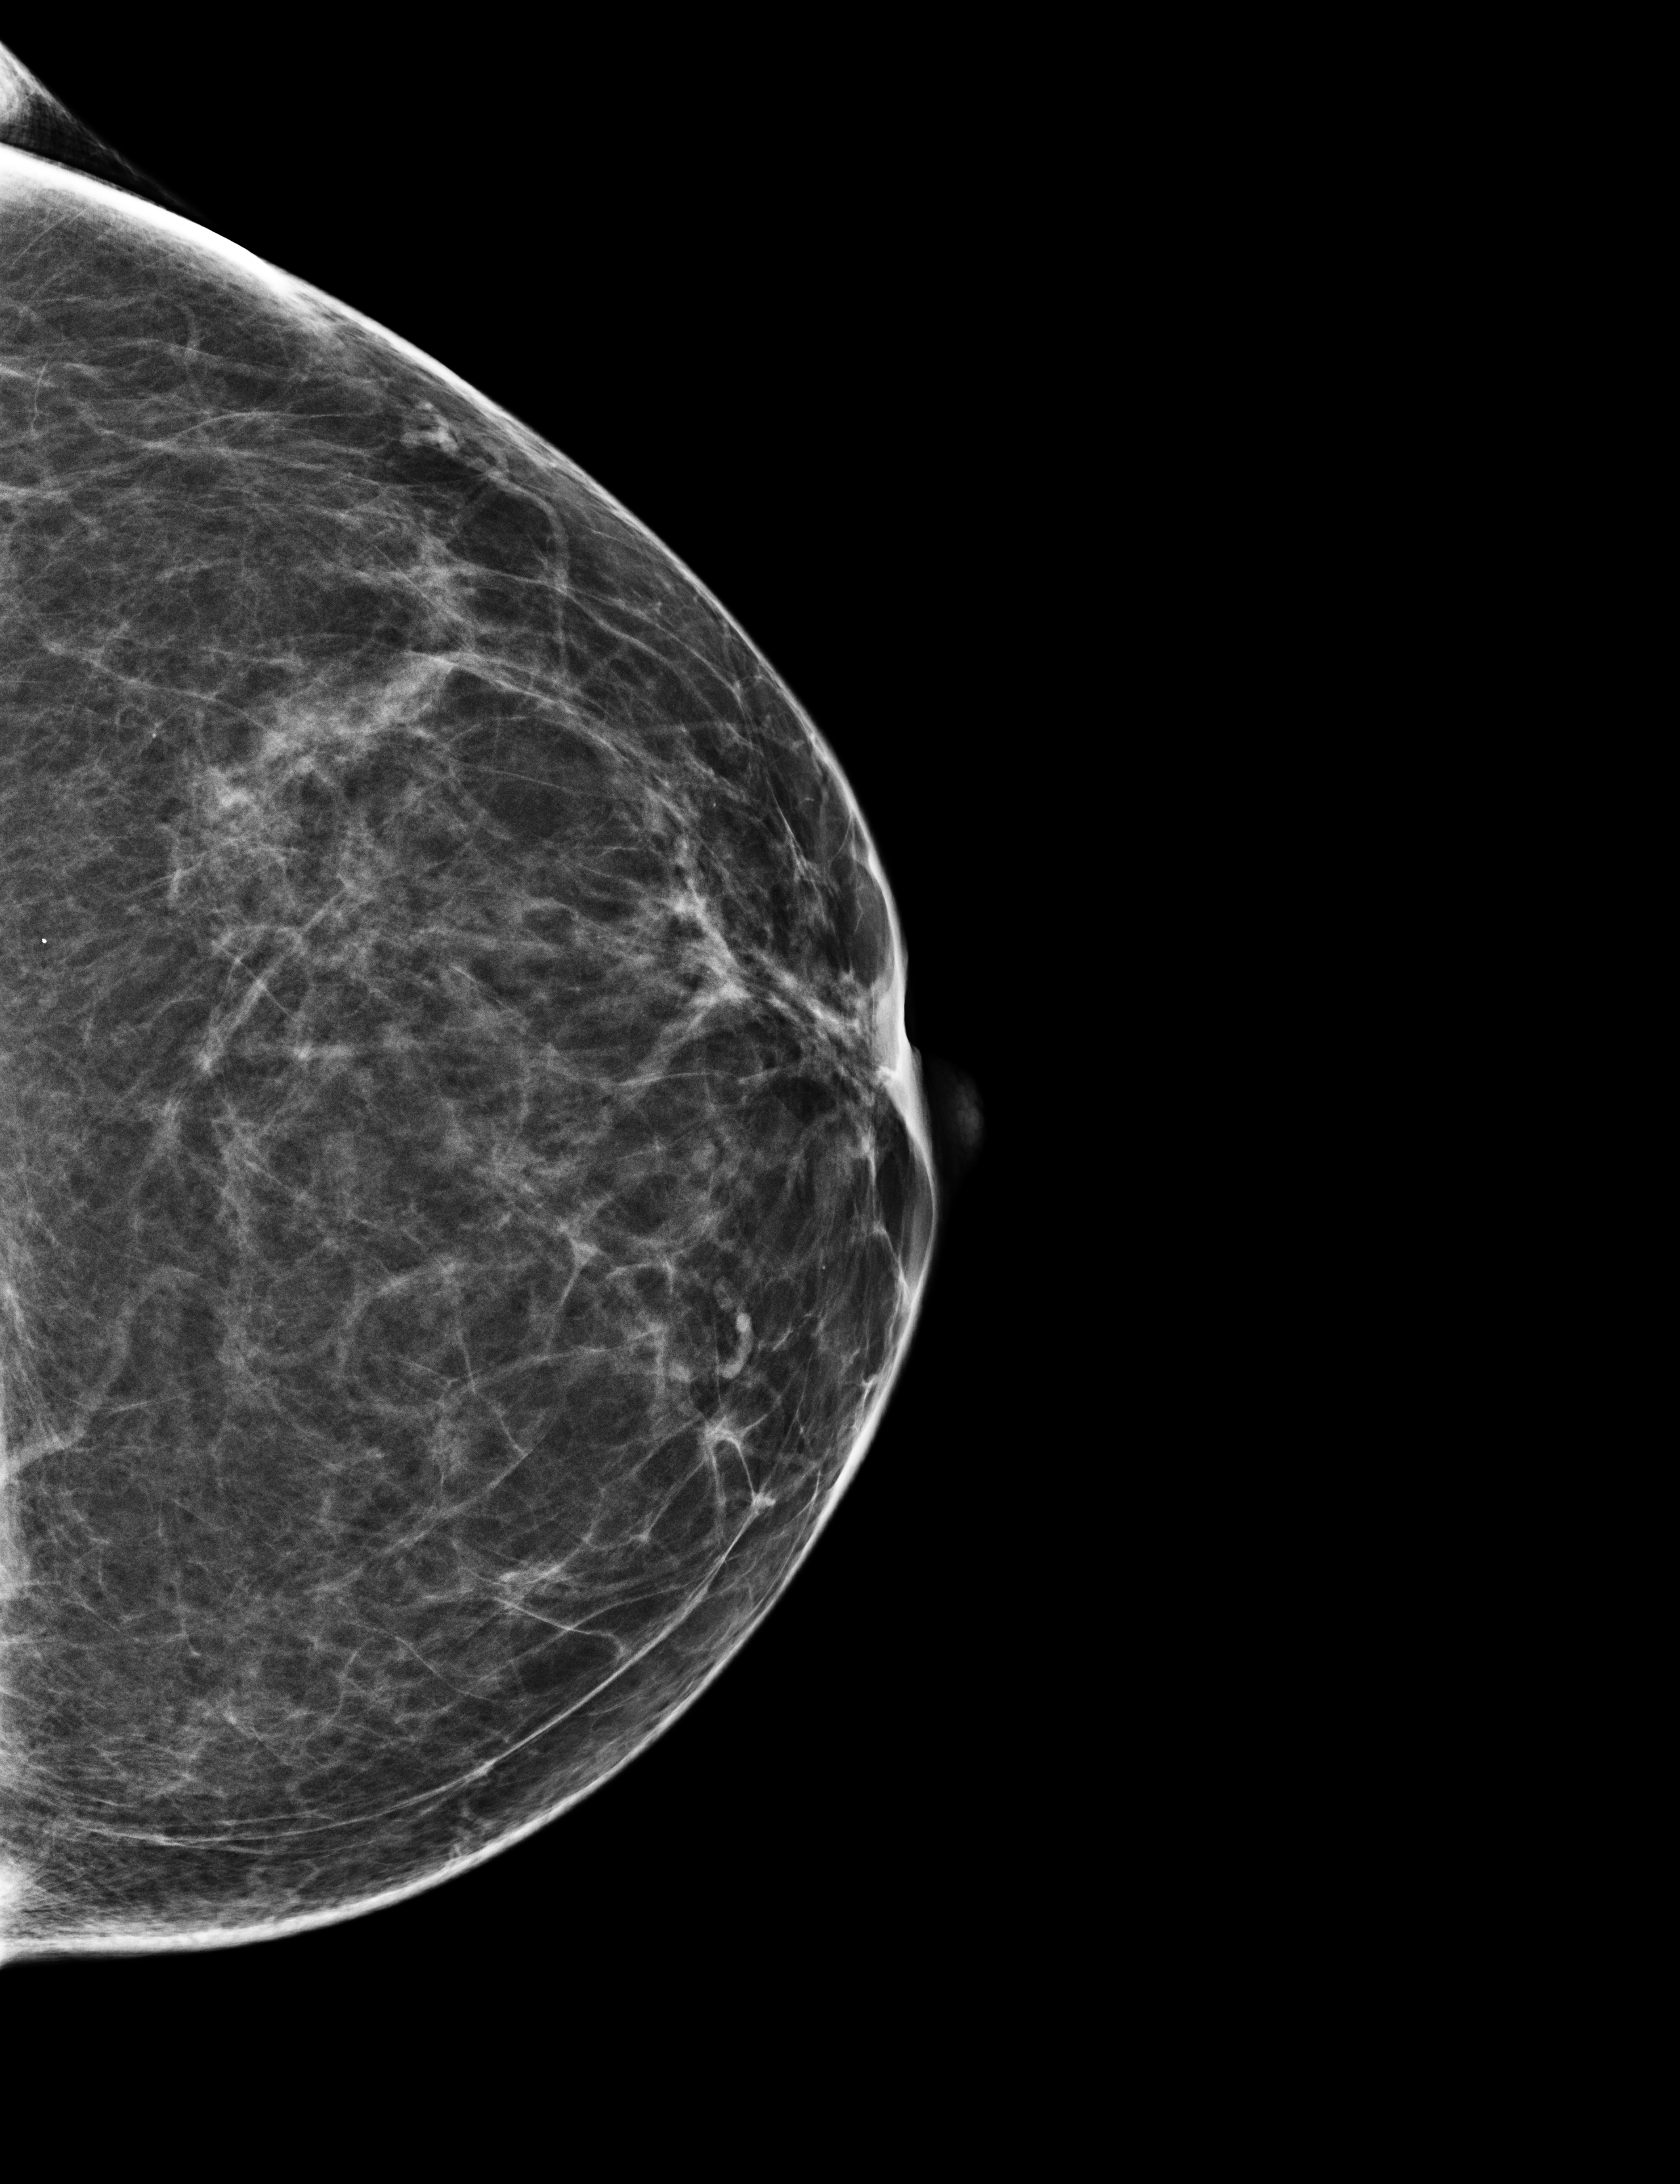
Screening examination, system: Selenia Dimensions. Patient: female, 55 years.
Image type: full-field digital mammogram. Breast: left. Projection: CC view.